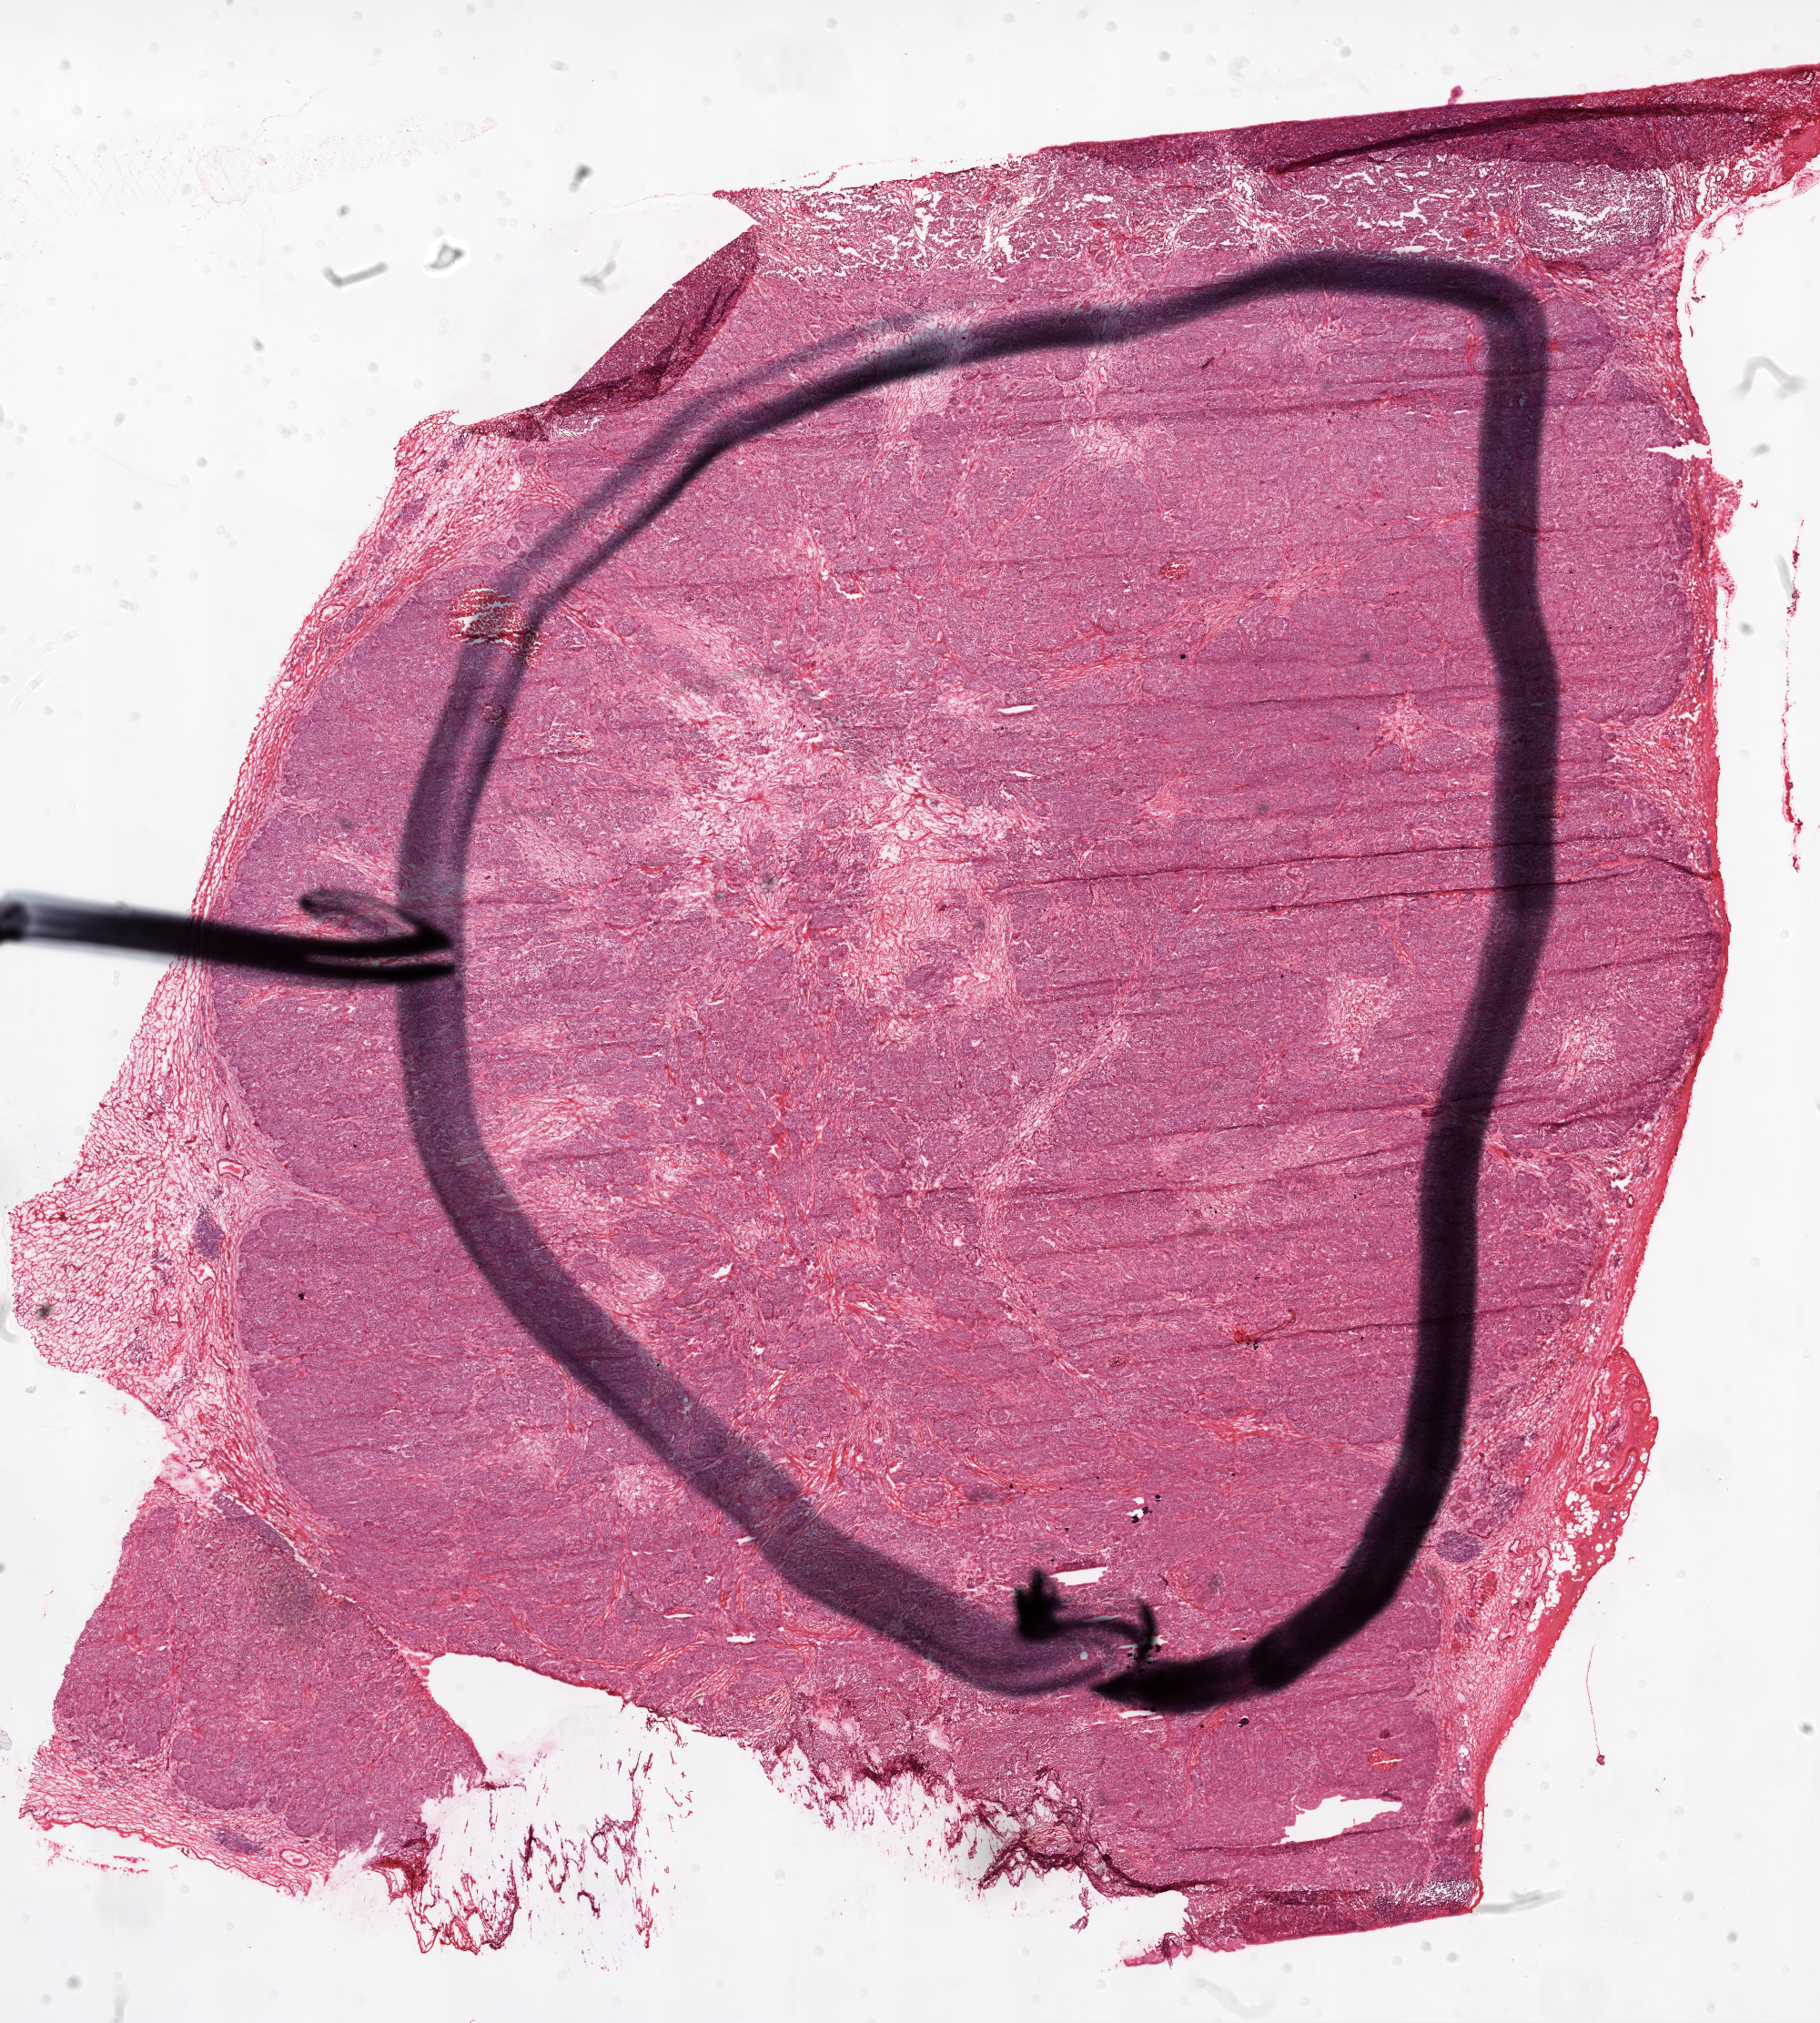
H&E-stained whole-slide image — a low-resolution overview of the entire scanned area, about 16.0 x 17.8 mm. Frozen section. Primary tumour sample from the ovary. Patient: female, age at initial diagnosis 47 years. Composition of this section per pathologist review: tumour cells 85%, tumour nuclei 90%.
Pathologic diagnosis: Serous cystadenocarcinoma, NOS.